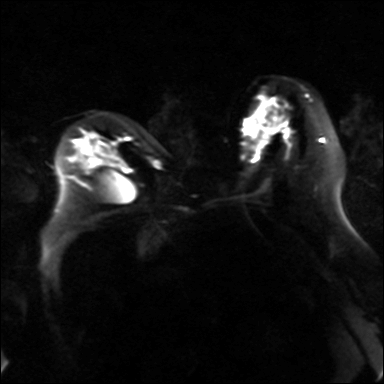
Breast MRI, one axial slice; slice 18 of 36 in the series (ordered by position); diffusion-weighted series; image 2 of 4 stored at this slice position (different b-values; order by instance number); 3 T; 4 mm slice thickness; 384 × 384 image matrix, field of view 320 × 320 mm. Female patient.
Annotated regions visible in this slice (manually delineated by an expert):
- tumour on diffusion-weighted imaging: box from (x=259, y=108) to (x=278, y=129) px